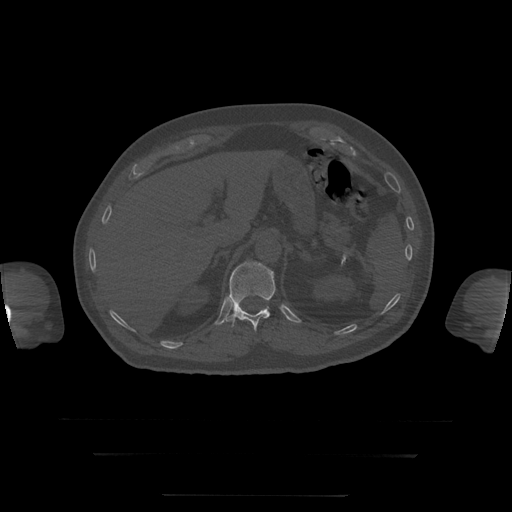
CT including the spine, one axial slice; slice 74 of 397 in the series (ordered by position); reconstruction kernel STANDARD; bone window (W 1800 / L 400 HU); 1.25 mm slice thickness; 512 × 512 image matrix, field of view 510 × 510 mm. Patient age 73 years. Case-level facts recorded for this patient, not image findings: primary cancer: prostate.
Structures marked on this image (semi-automatically segmented with operator editing):
- T12 vertebra: bounding box <227,262,276,332> (left, top, right, bottom; pixels)